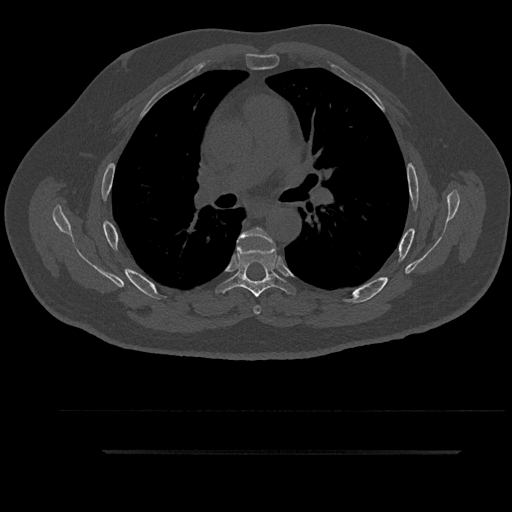
CT including the spine, one axial slice. Slice 590 of 797 in the series (ordered by position). Reconstruction kernel Br40s/3. Bone window (W 1800 / L 400 HU). 0.5 mm slice thickness. 512 × 512 image matrix, field of view 432 × 432 mm. Patient: male, 63 years. From the clinical record (not read from this slice): primary cancer: renal; vertebrae with lytic lesions (as recorded): T8.
Outlined on this slice (semi-automatic segmentation, software-assisted and operator-edited):
- T5 vertebra: box from (x=237, y=227) to (x=274, y=314) px
- T6 vertebra: (x=220, y=238)–(x=290, y=297)